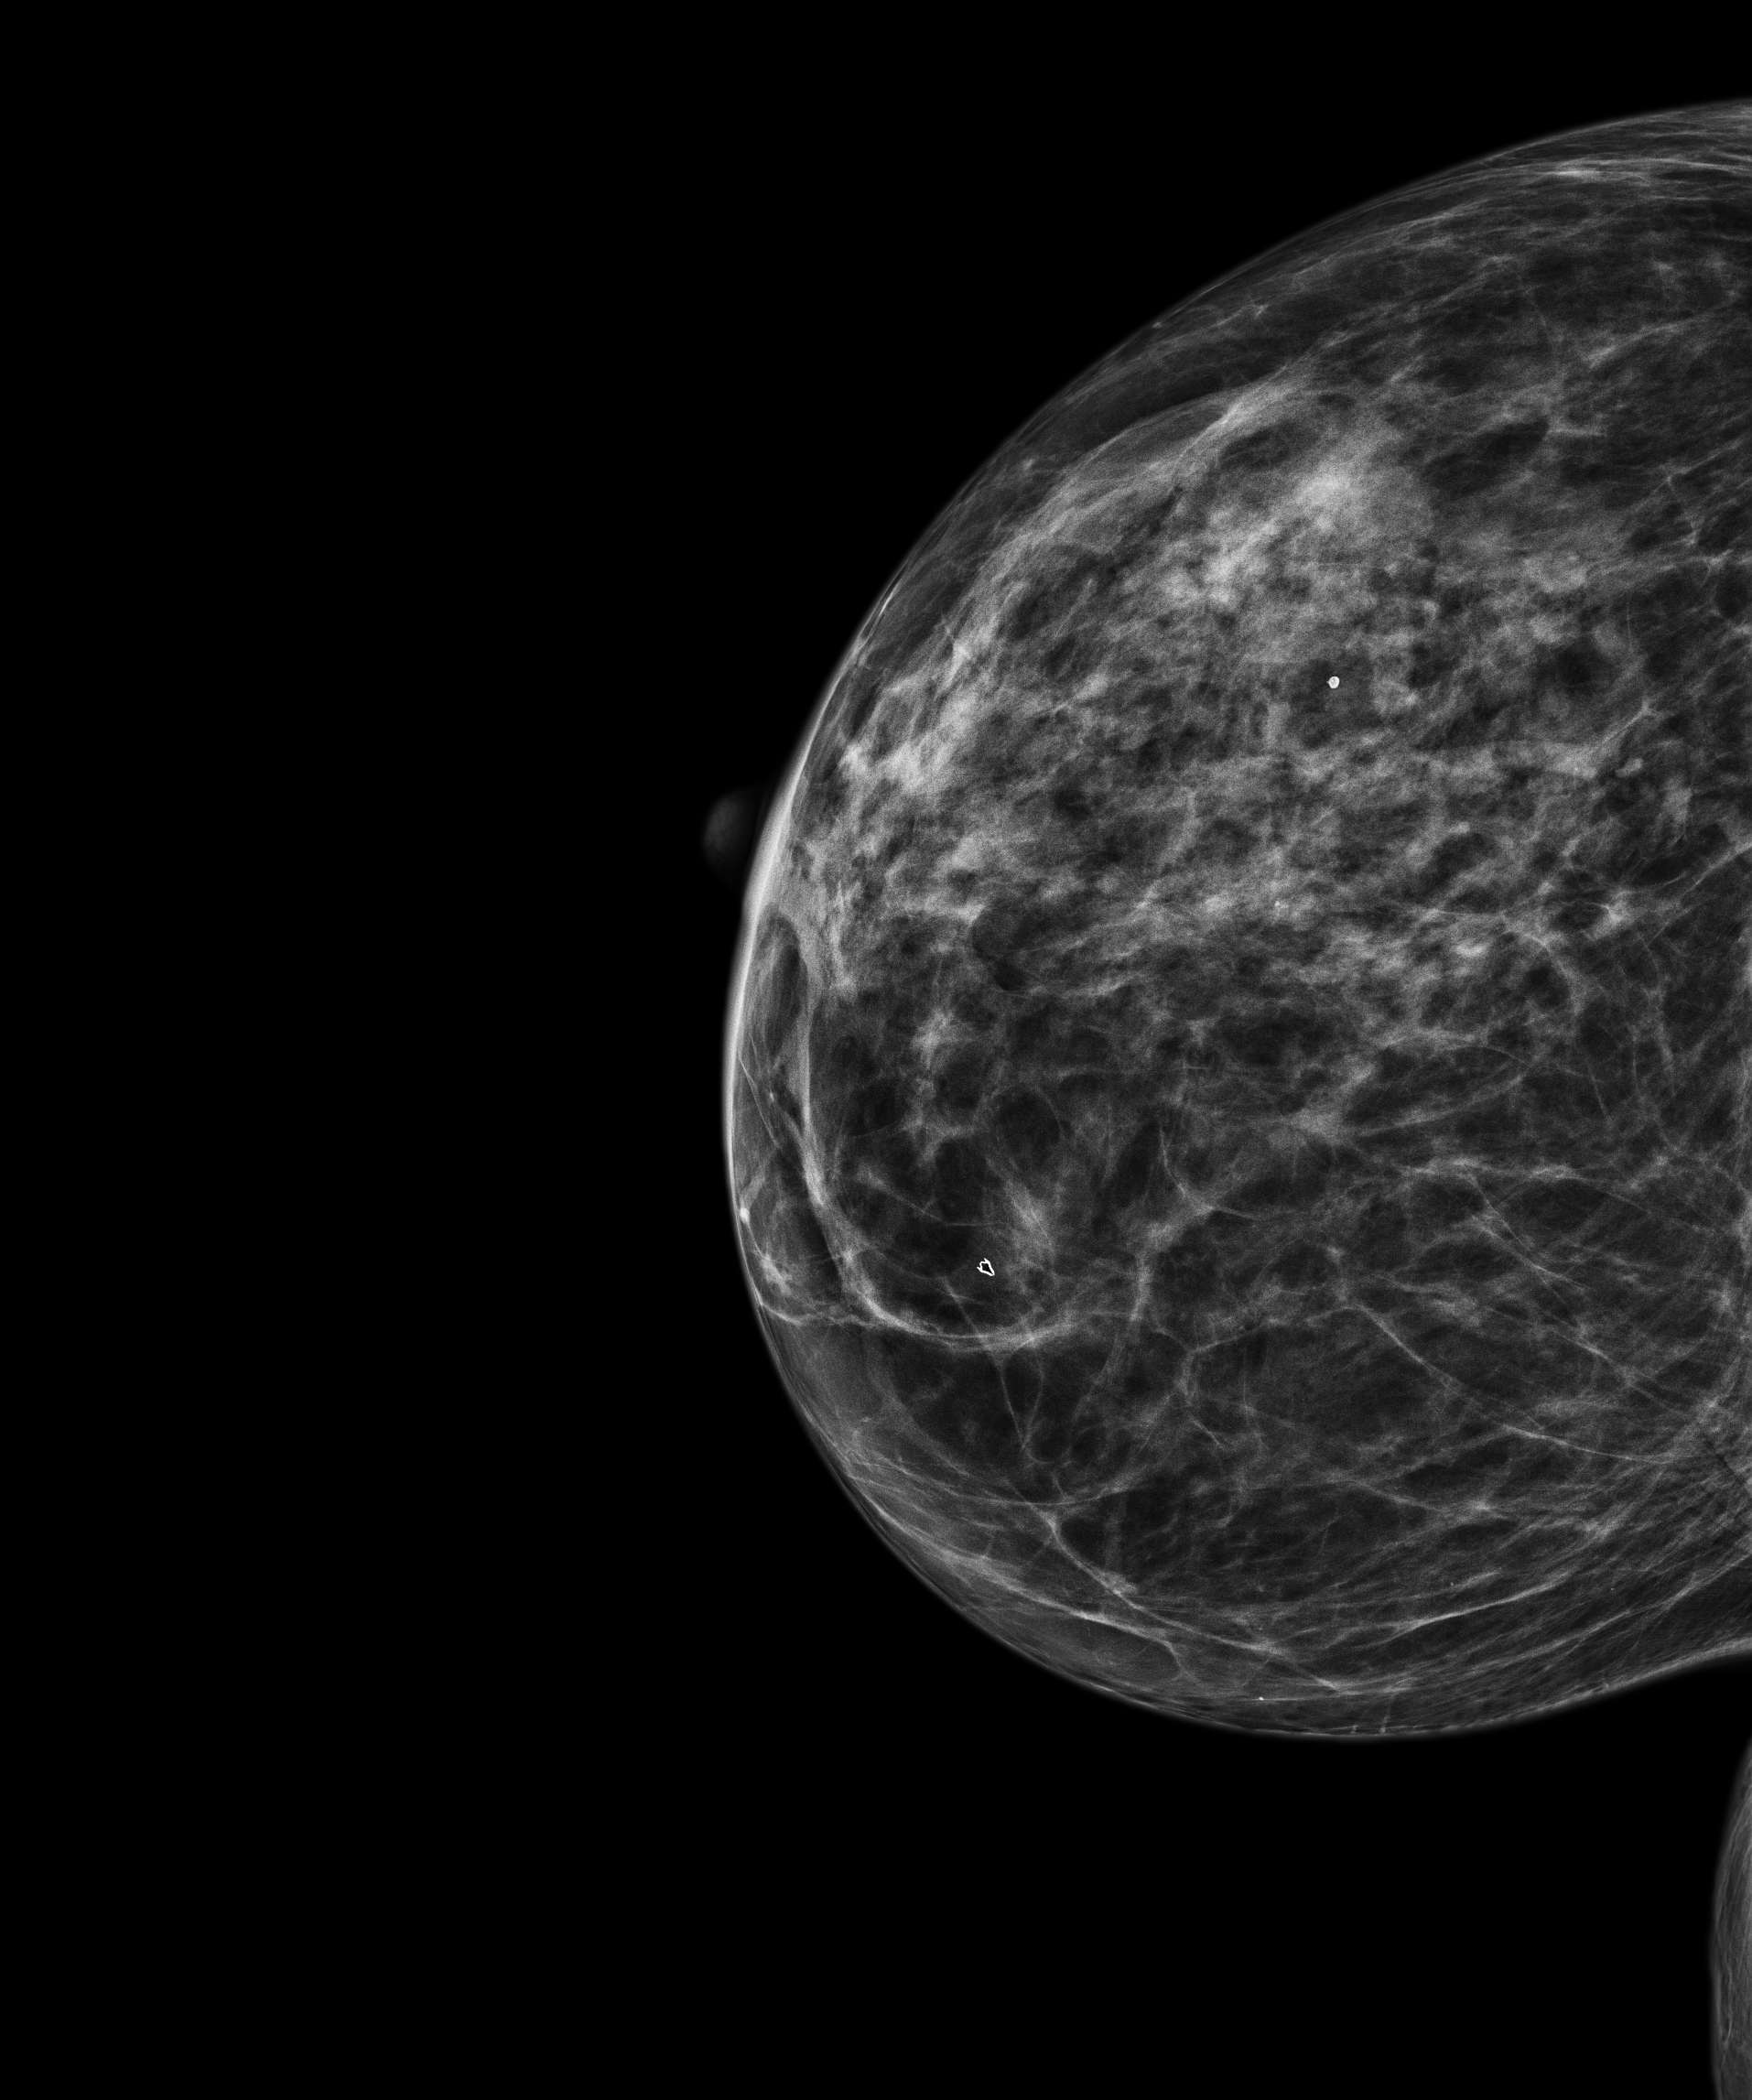
Annual screening mammography examination. Female patient, age 57 years.
Image type: full-field digital mammogram. Breast: right. Projection: CC view.